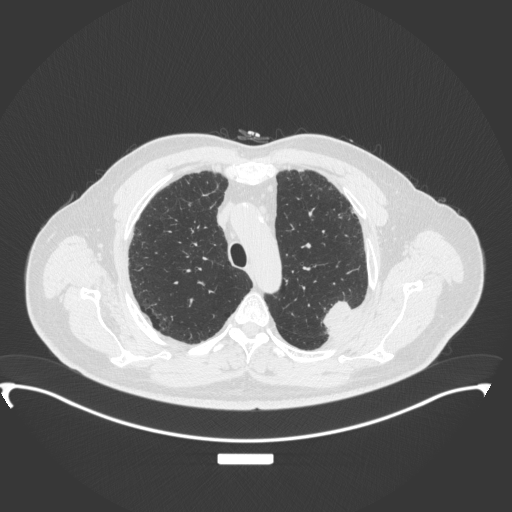
Chest CT, one axial slice; slice 277 of 350 in the series (ordered by position); reconstruction kernel B31f; lung window (W 1500 / L -600 HU); 512 × 512 image matrix, field of view 459 × 459 mm. Patient: male, 64 years. From the clinical record (not read from this slice): clinical TNM (as recorded): T1c N1 M1.
Annotated regions visible in this slice (bounding box drawn by a radiologist):
- lung tumour (recorded histology: adenocarcinoma): bounding box <319,298,352,333> (left, top, right, bottom; pixels)